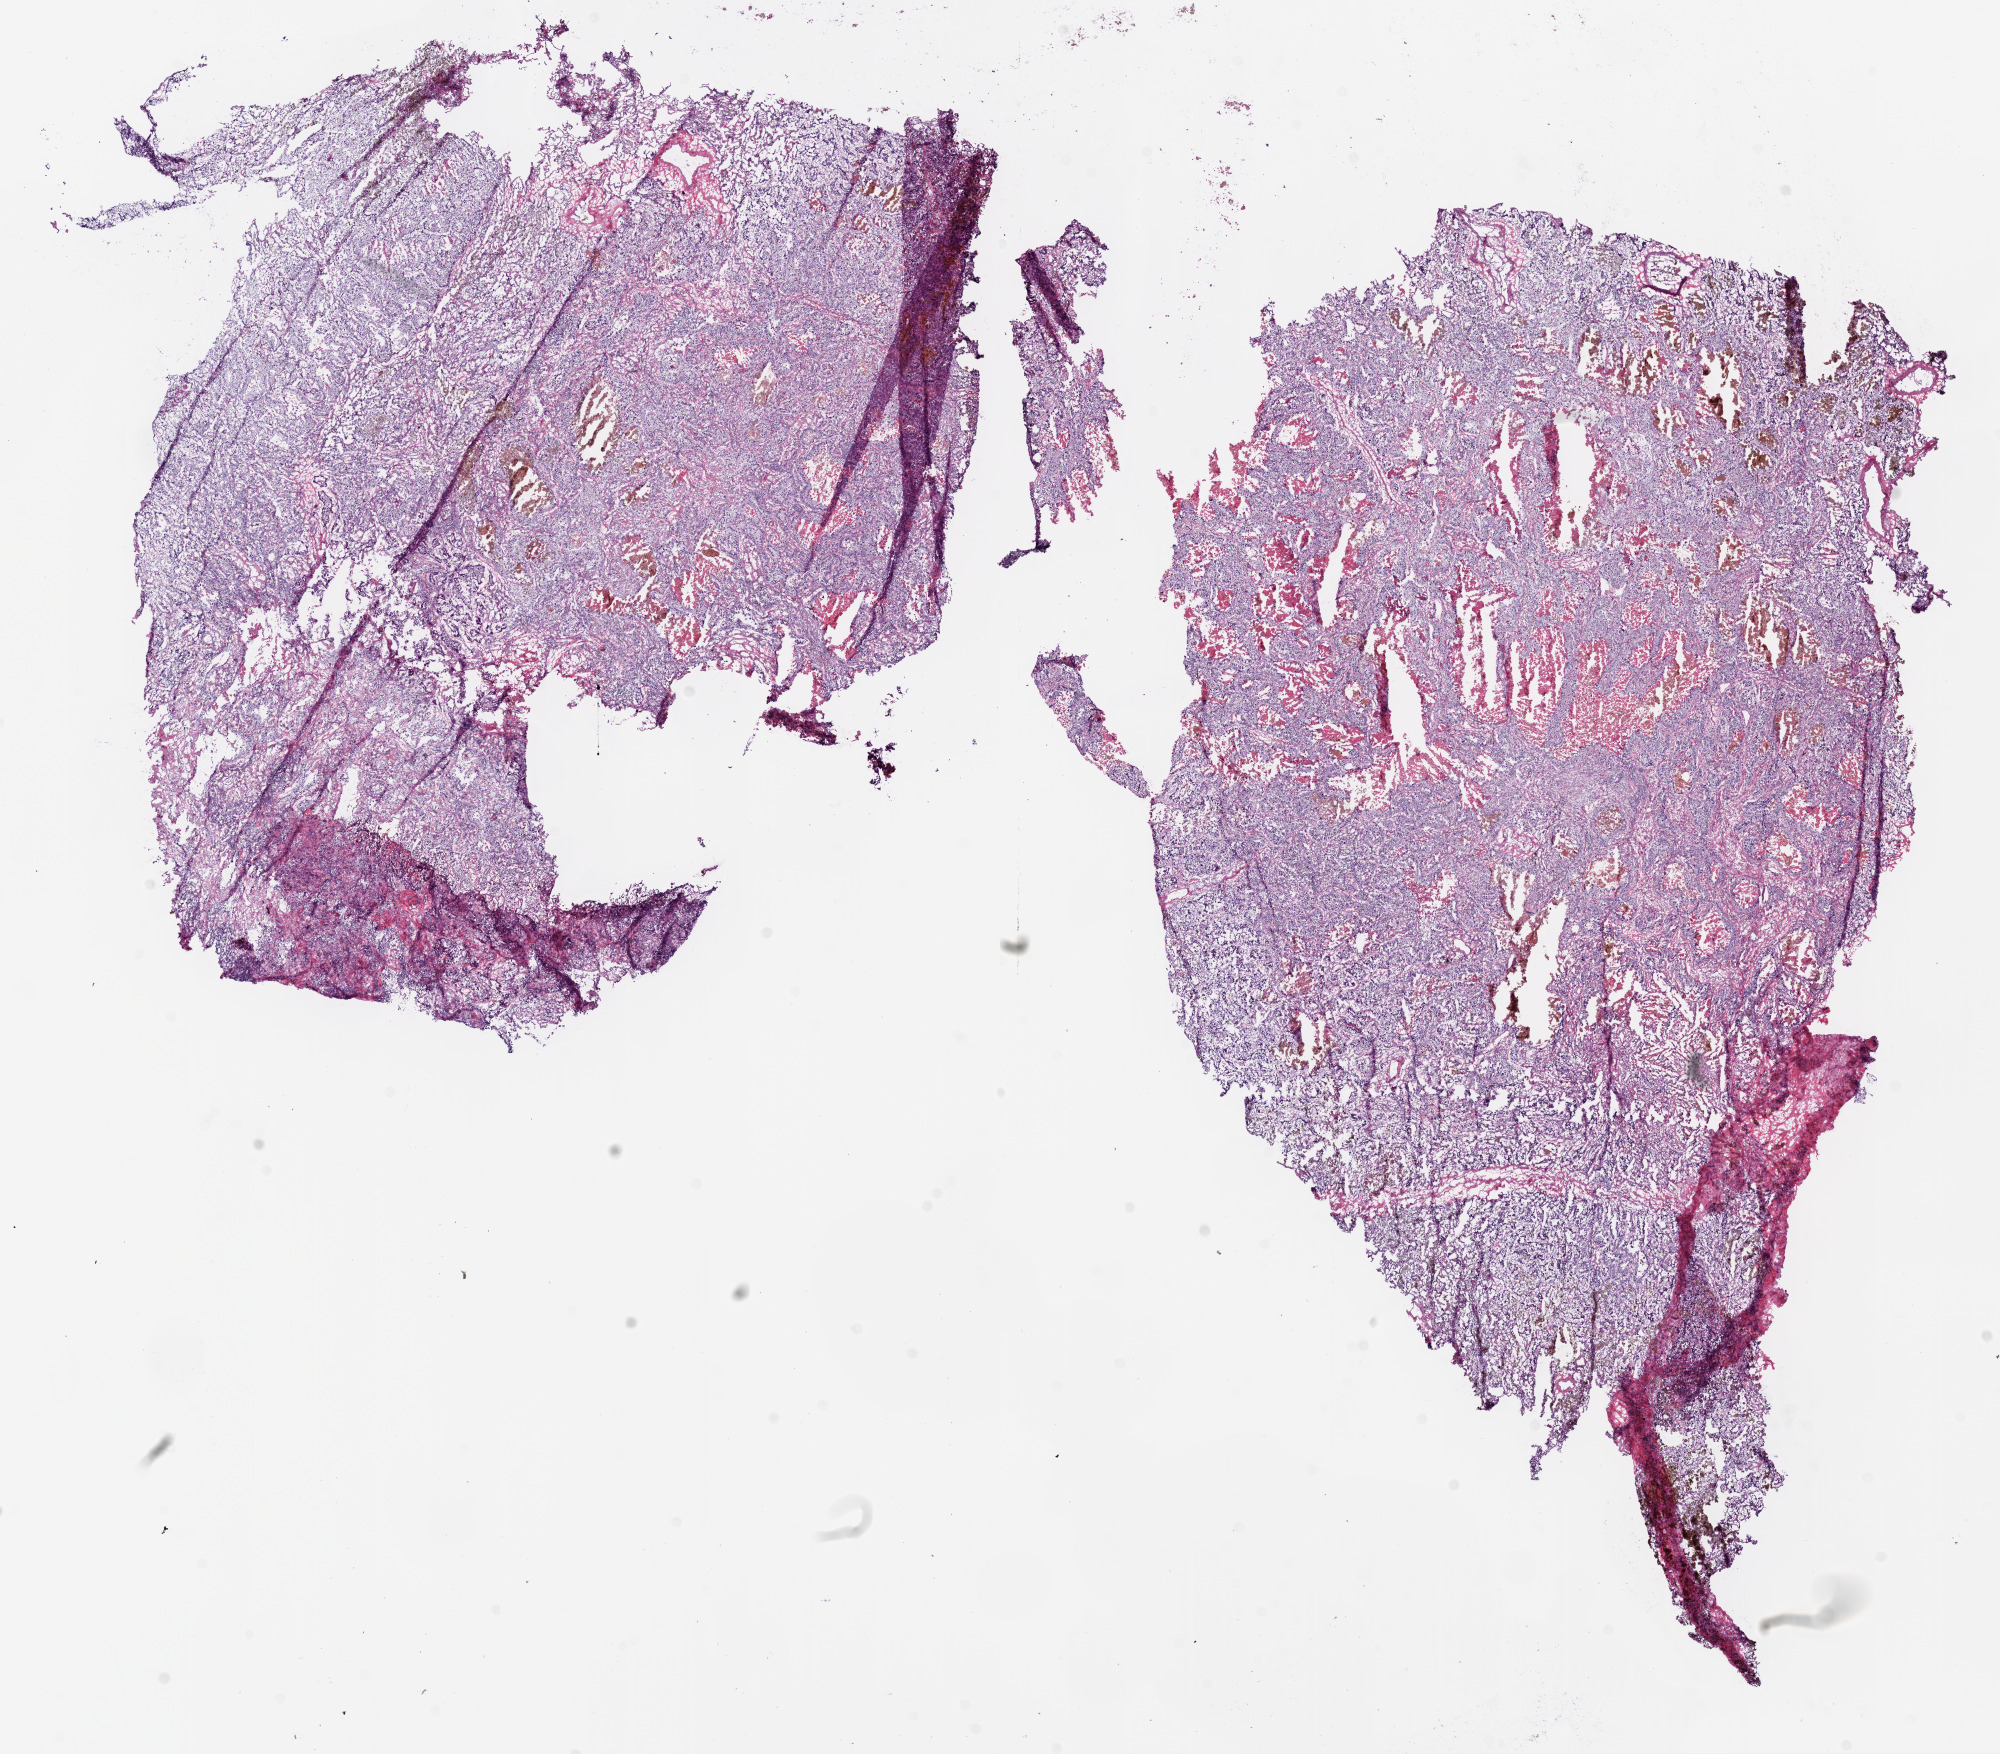
Whole-slide histology image, H&E-stained, low-resolution overview of the scanned area, about 16.0 x 14.1 mm (acquisition: 20x scan), frozen section from the bottom of the tissue portion, primary tumour sample from the lung. Male, age 65 years at initial diagnosis. Pathologist review of this section (percent, as recorded): tumour cells 75%, tumour nuclei 80%, normal cells 0%, stromal cells 10%, necrosis 15%.
• laterality: left
• TNM: T2 N0 M0
• AJCC pathologic stage: IA
• diagnosis: Adenocarcinoma, NOS (upper lobe, lung)